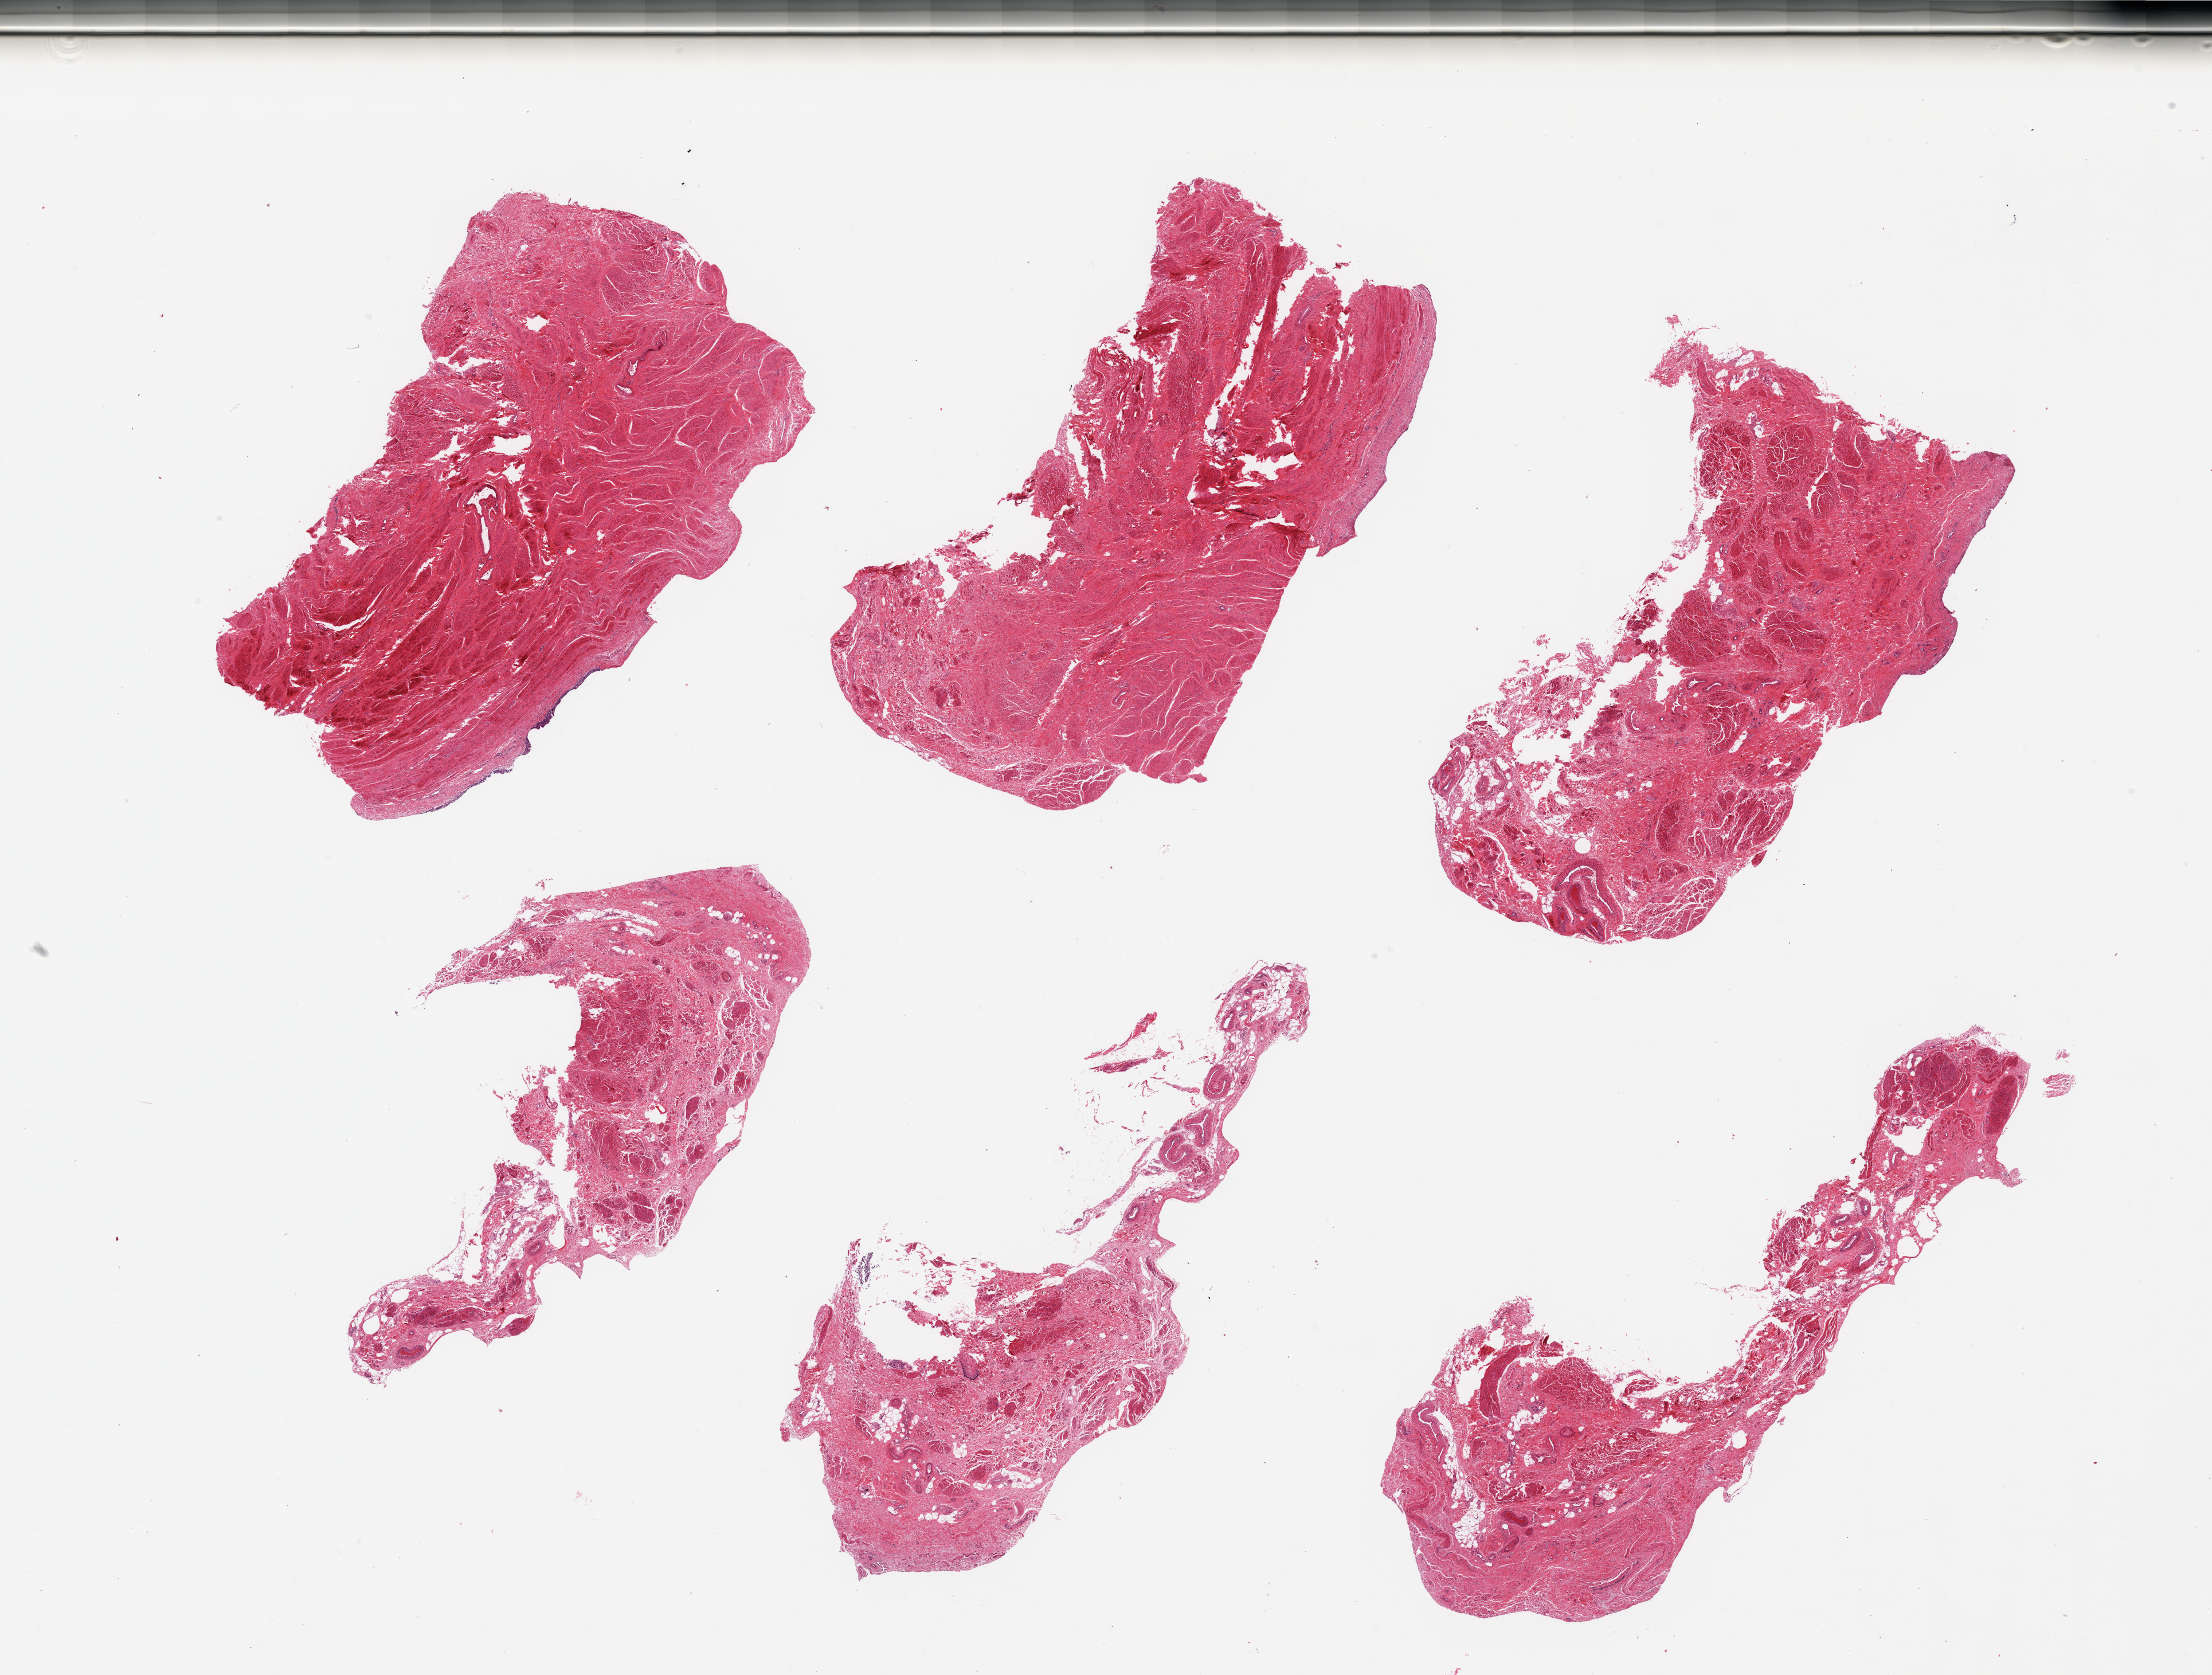
Hematoxylin and eosin (H&E) whole-slide image — low-resolution overview of the scanned area, about 30.5 x 23.1 mm (acquisition: 20x scan), PAXgene-fixed paraffin-embedded (PFPE) section, sampled site (target tissue): vagina, tissue donor sample. Donor sex: female.
Review note (as recorded): 6 pieces; fibromuscular tissue with vessels, nerves and fat and focal trace of residual epithelium.